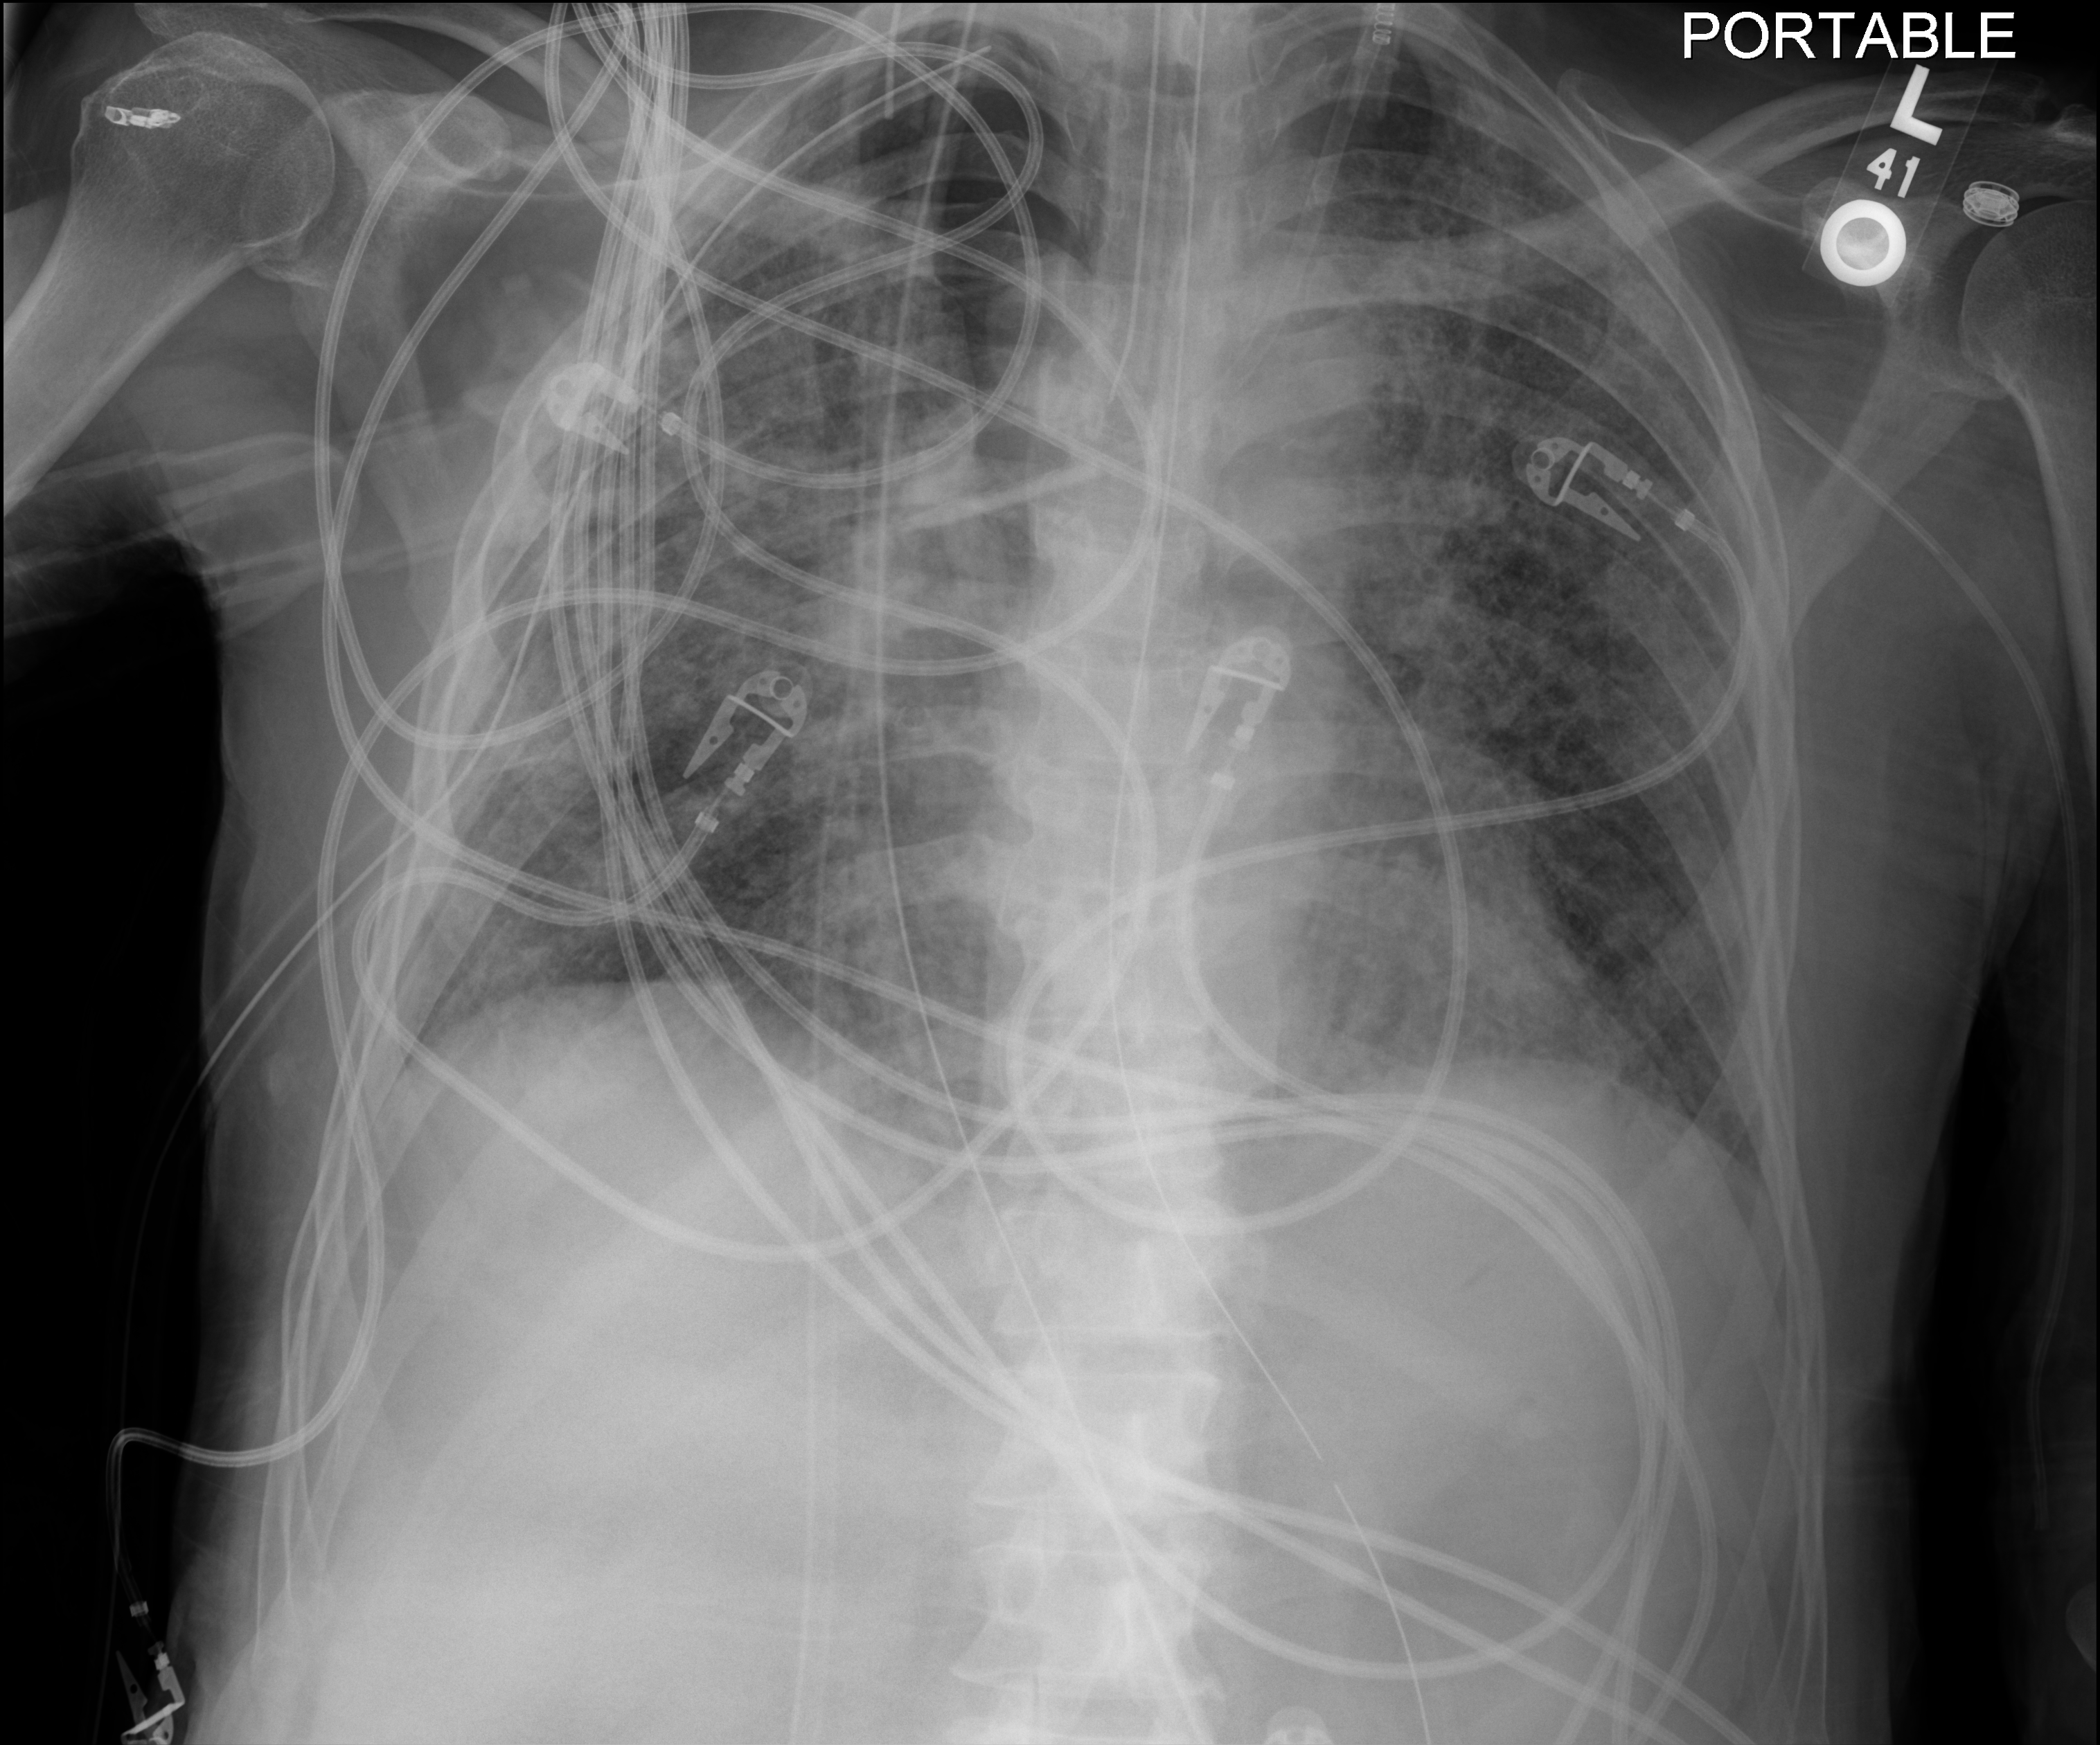
Chest X-ray. Patient hospitalised with COVID-19; male, aged 60–74 years.
Admission-level facts for this patient (not findings on this image; timing relative to this image not recorded):
- COPD (admission record): no
- admitted to intensive care during this hospital stay: yes